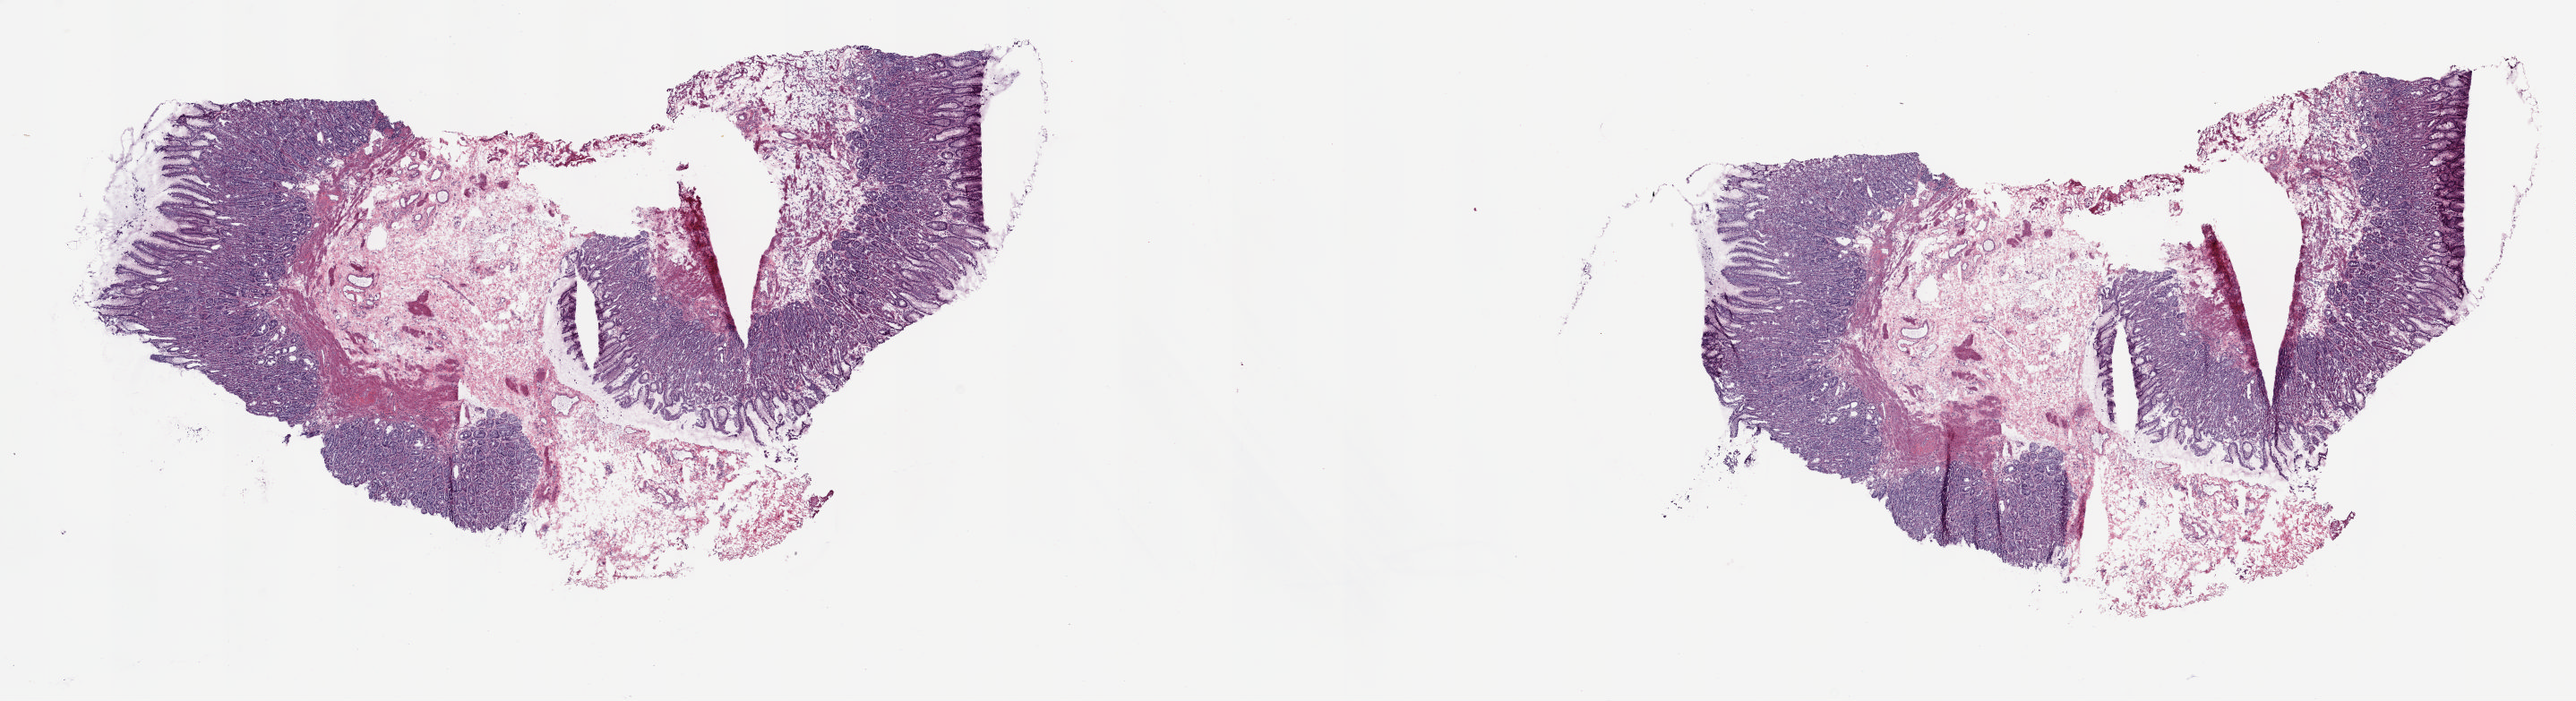
Digitized H&E tissue section (whole slide), a low-resolution overview of the entire scanned area, about 22.8 x 6.2 mm. Frozen section. Solid tissue normal (non-tumour tissue) sample from the esophagus. Male patient; age at initial diagnosis 81 years.
This section: solid tissue normal sample (biorepository sample class). Patient diagnosis: Adenocarcinoma, NOS (lower third of esophagus).